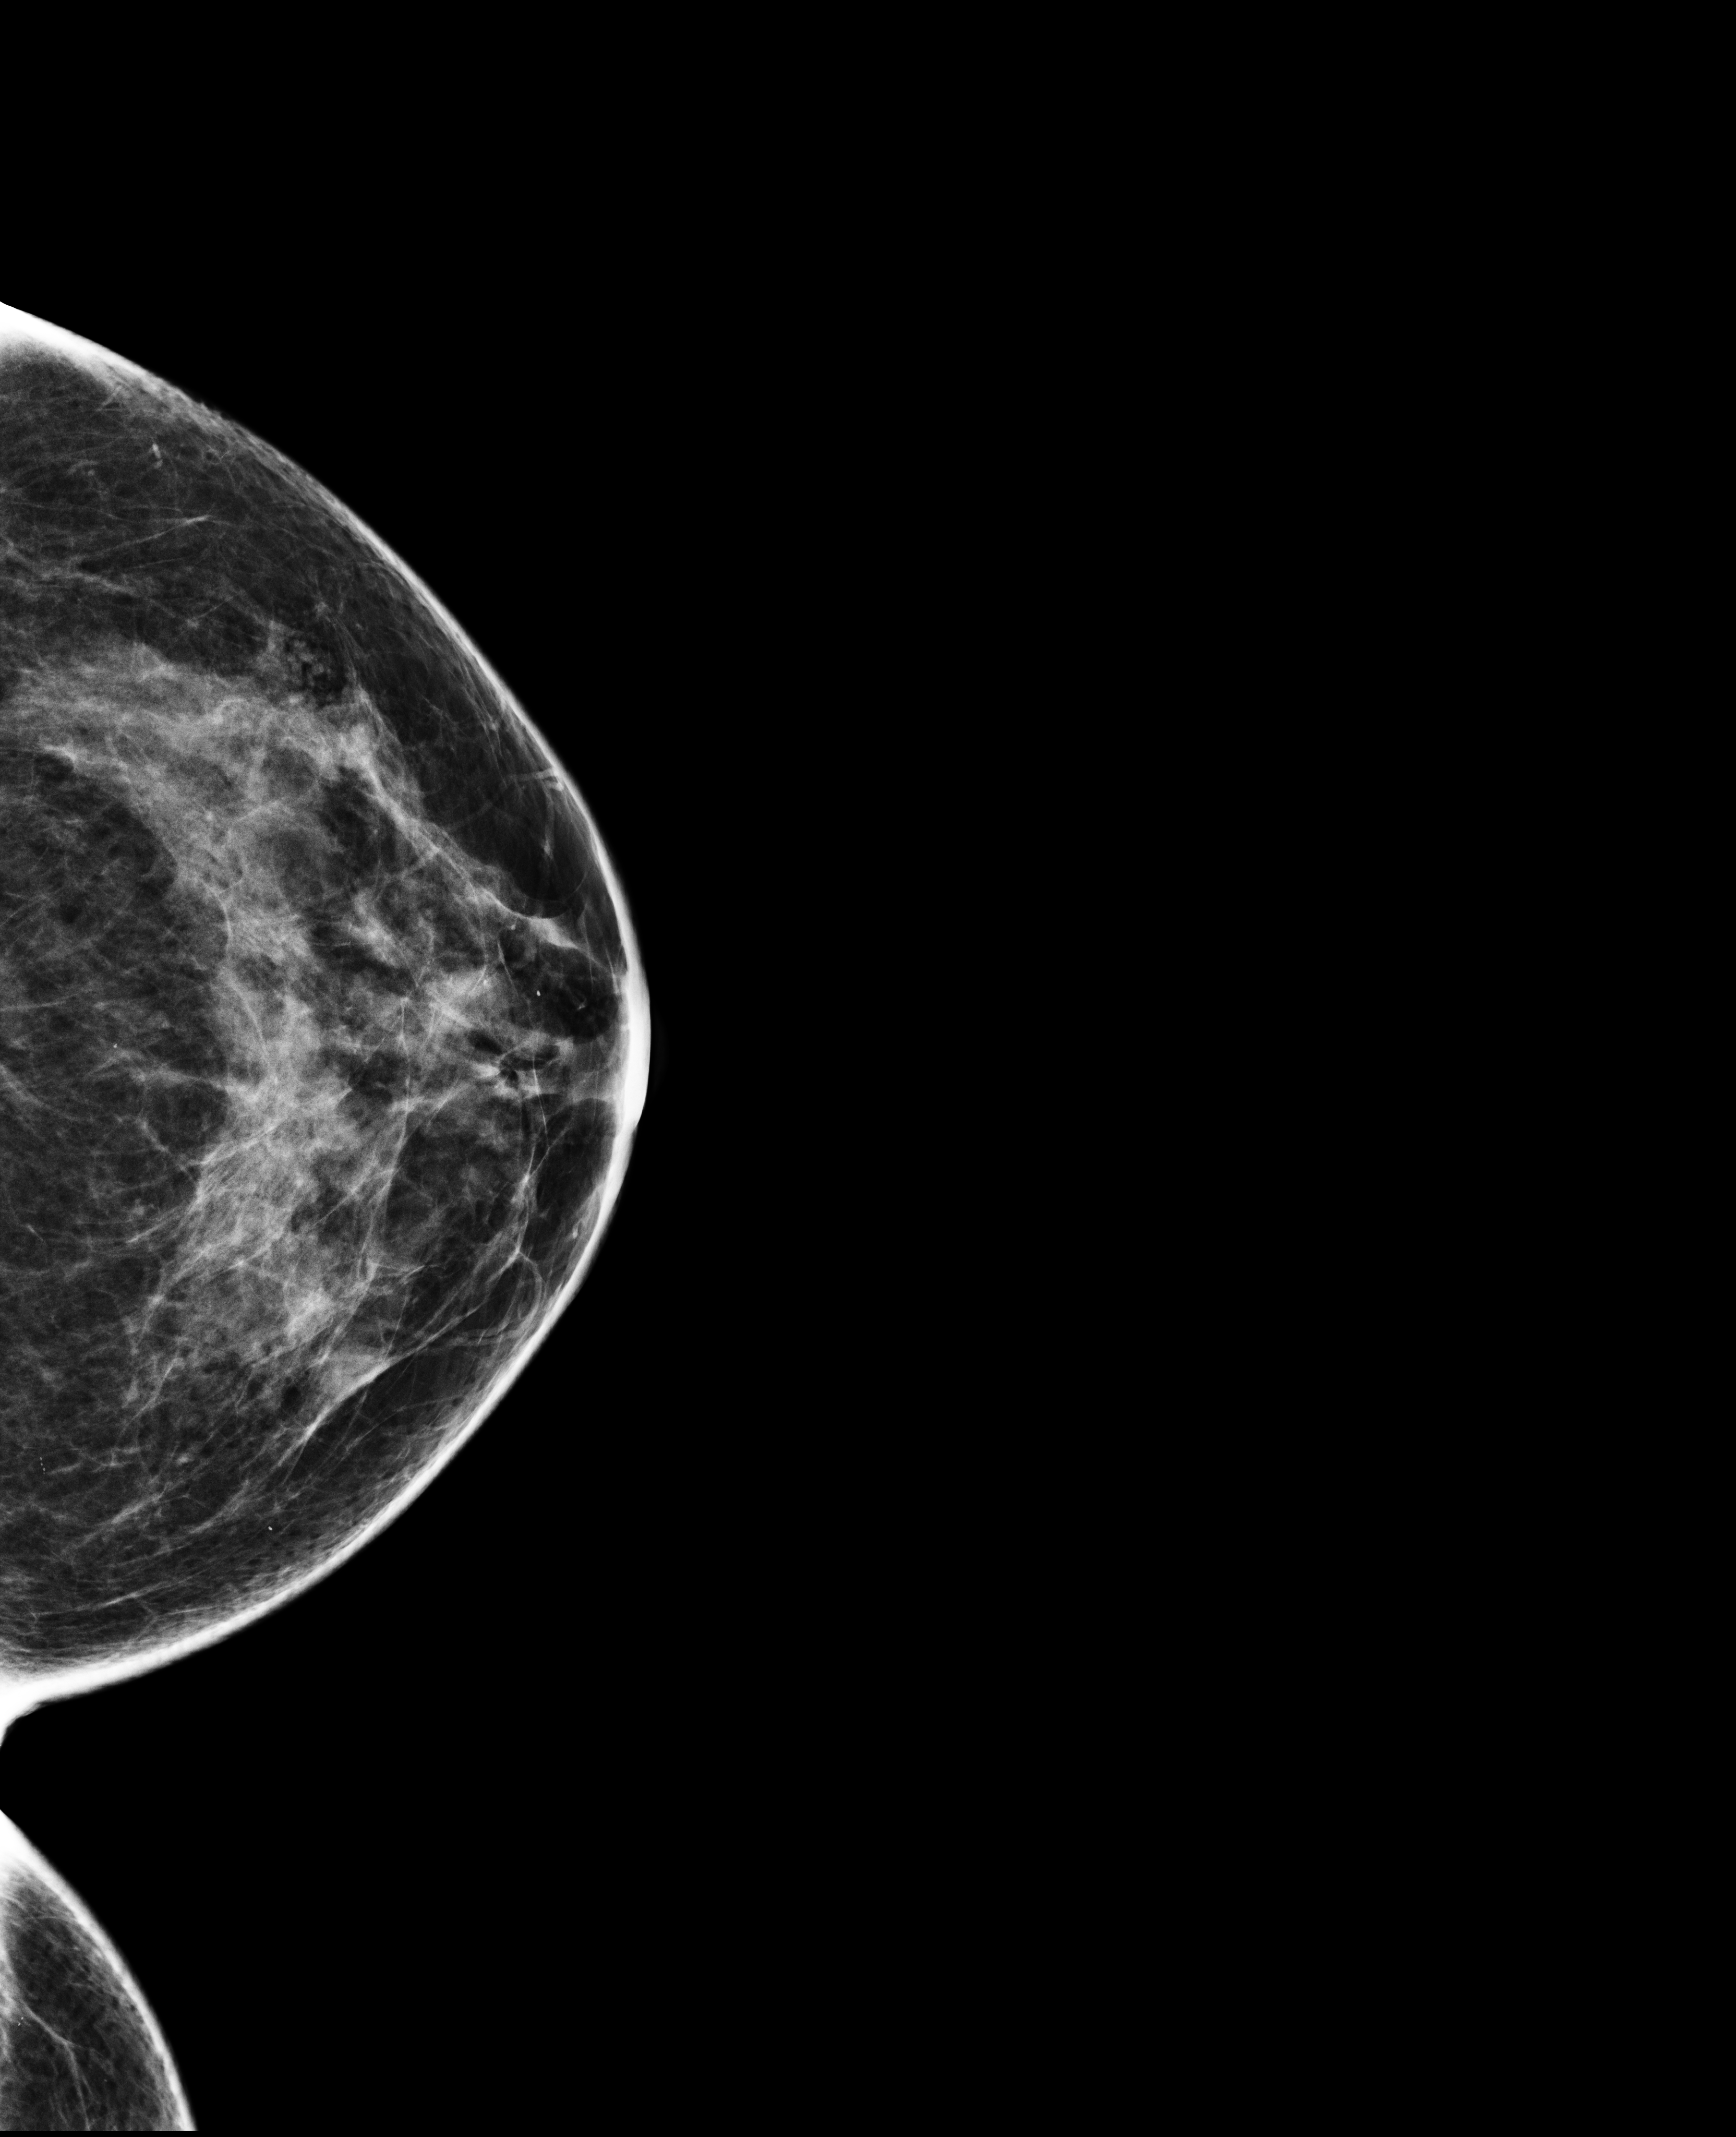
Annual screening mammography examination. Patient aged 47 years (female).
Image type: full-field digital mammogram. Breast: left. Projection: craniocaudal (CC) view.